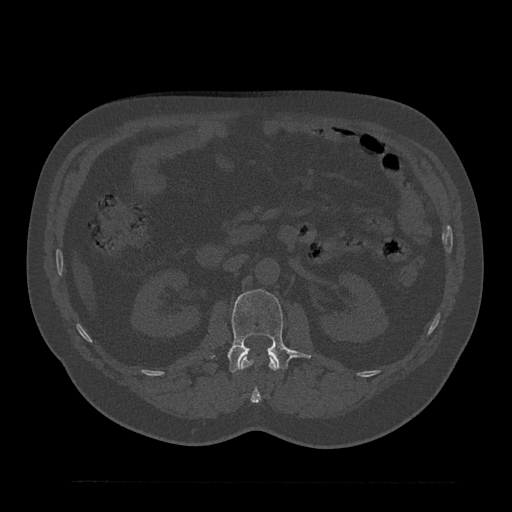
CT including the spine, one axial slice. Position 117 of 797 along the scan axis. Reconstruction kernel Br40s/3. 120 kVp. Bone window (W 1800 / L 400 HU). 0.5 mm slice thickness. 512 × 512 image matrix, field of view 430 × 430 mm. Male patient, age 61 years. From the clinical record (not read from this slice): primary cancer: prostate.
Structures marked on this image (semi-automatically segmented with operator editing):
- L1 vertebra: bounding box (x1, y1, x2, y2) in pixels: (241, 354, 277, 403)
- L2 vertebra: (228, 289, 310, 373)